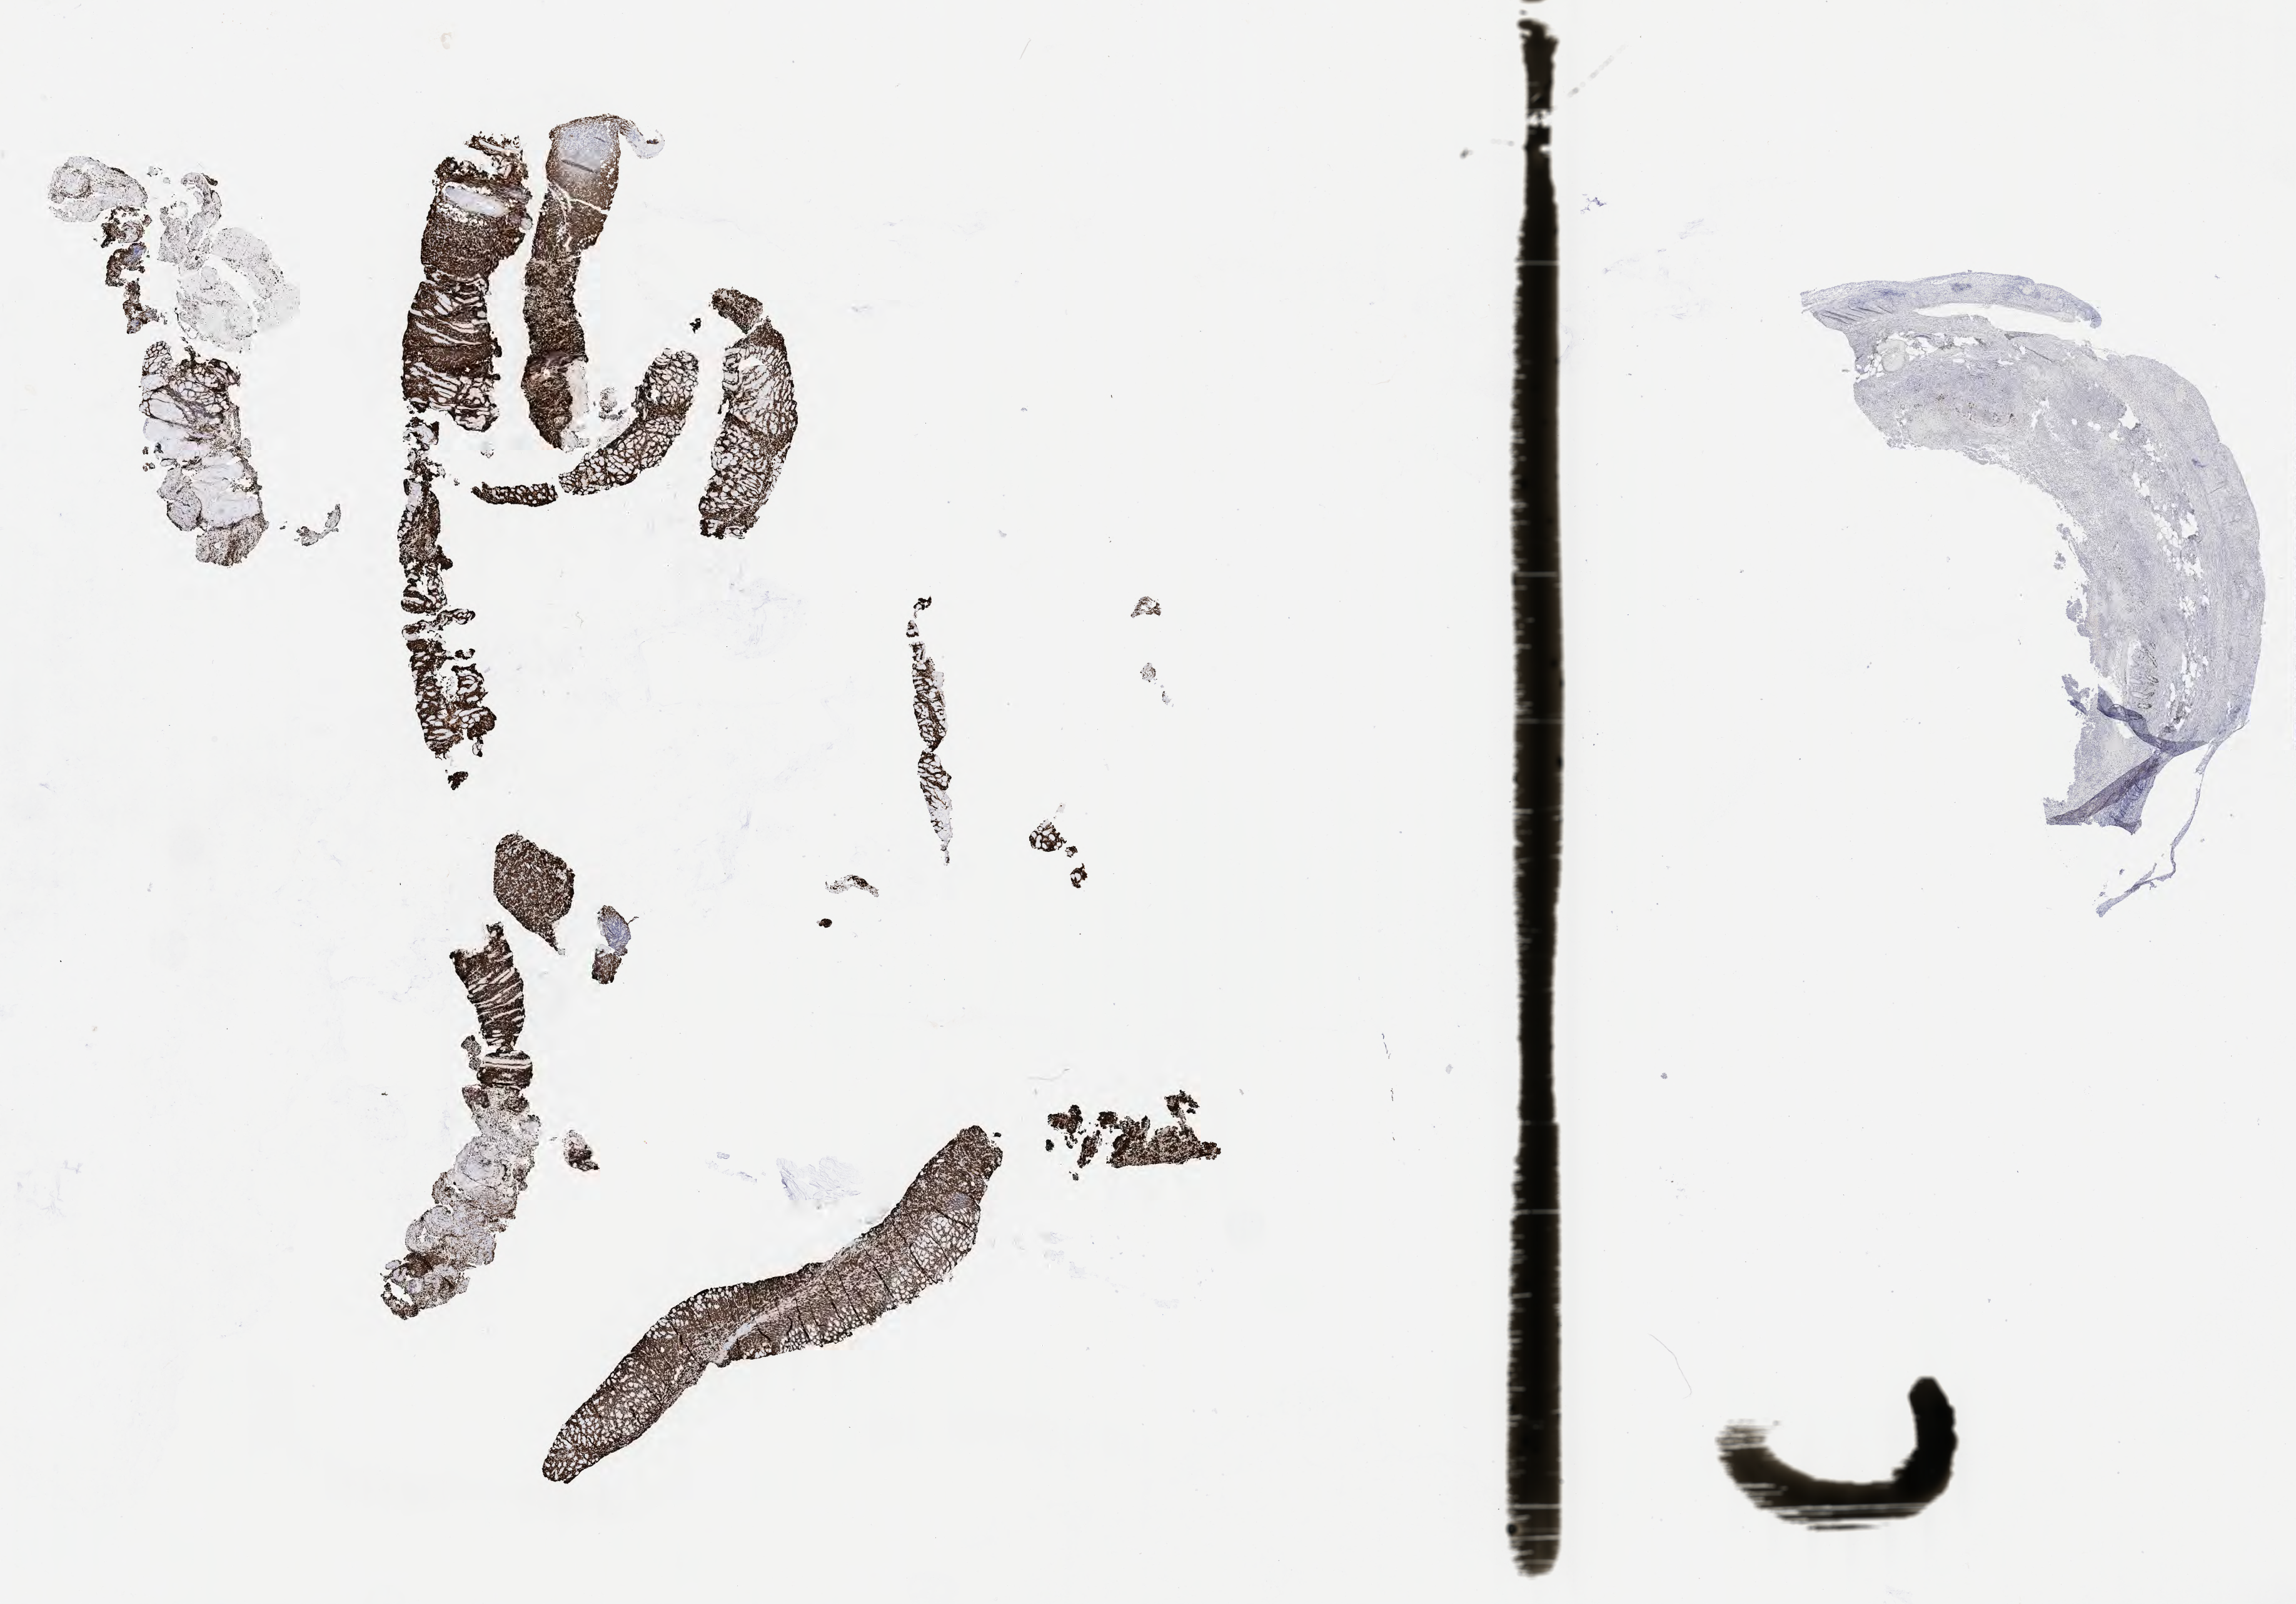
IHC for Ki-67, whole-slide image — a low-resolution overview of the entire scanned area, about 29.7 x 20.7 mm, tumor tissue, site: bone of pelvis. Male patient, 53 years old.
* diagnosis: Burkitt lymphoma, NOS